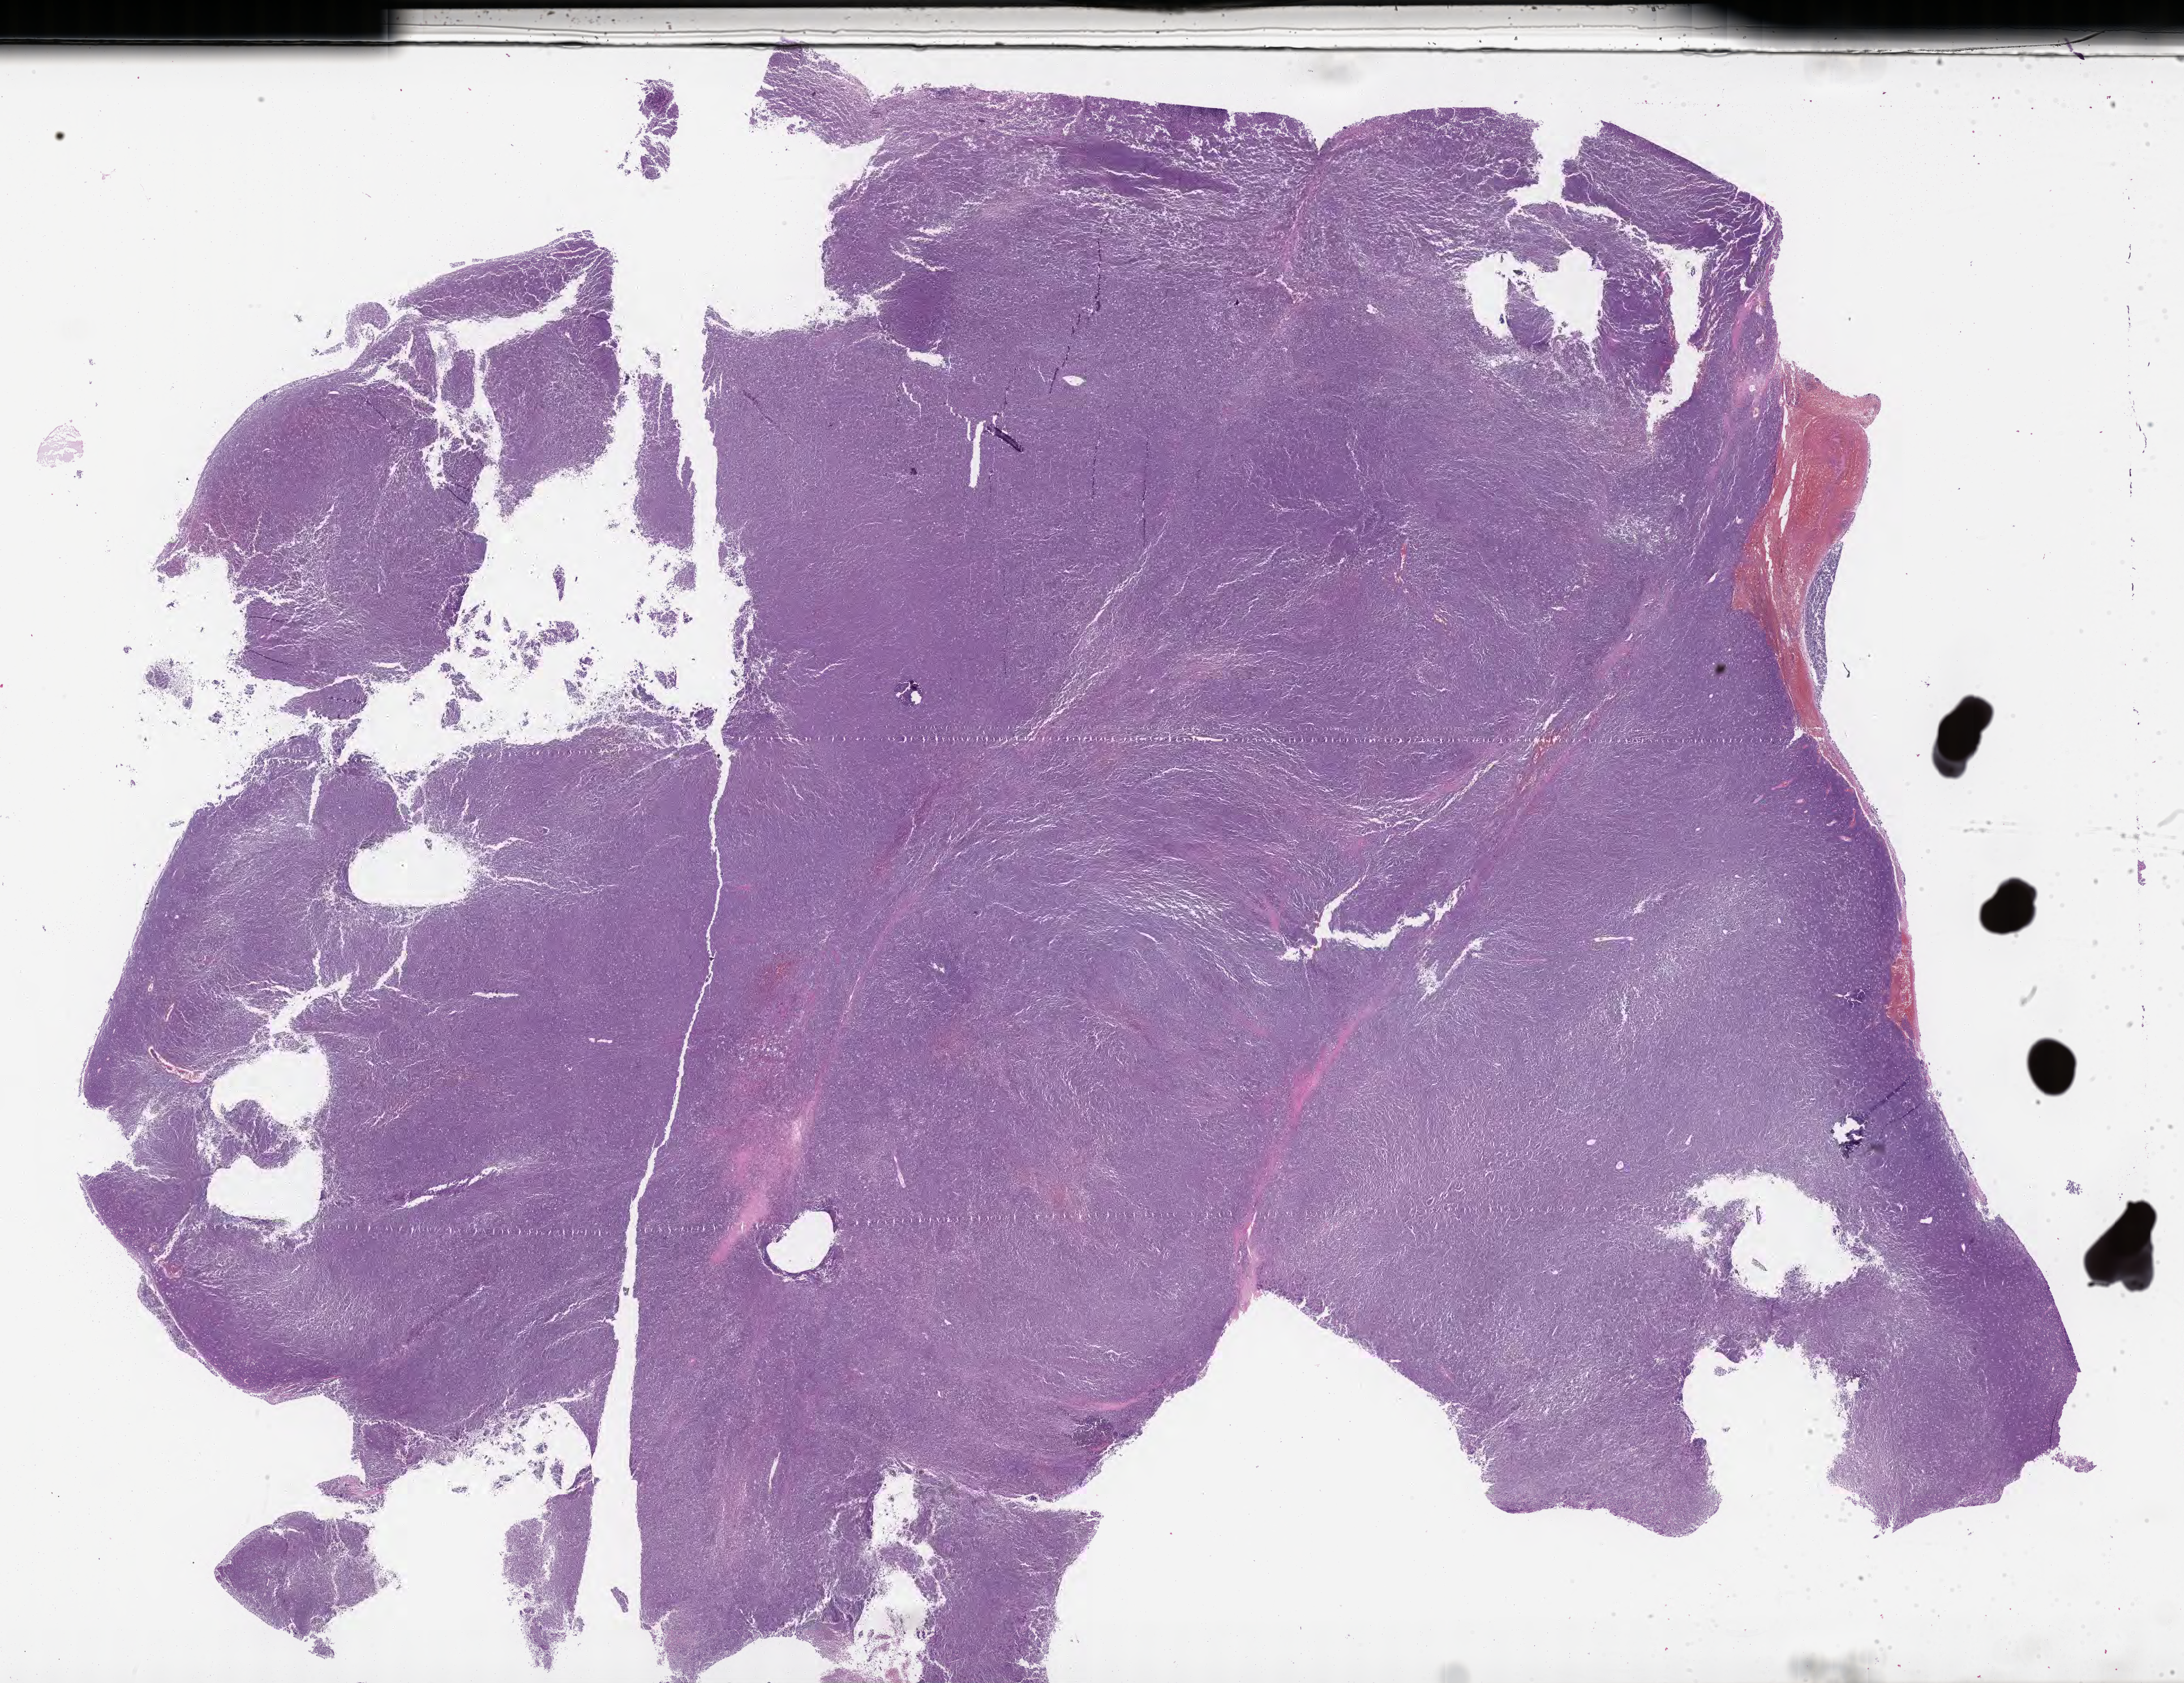
H&E whole-slide image — shown as a low-resolution overview of the whole scanned area (about 31.2 x 24.0 mm); tumor tissue. Male patient, age 15 years.
Diagnosis: Burkitt lymphoma, NOS.